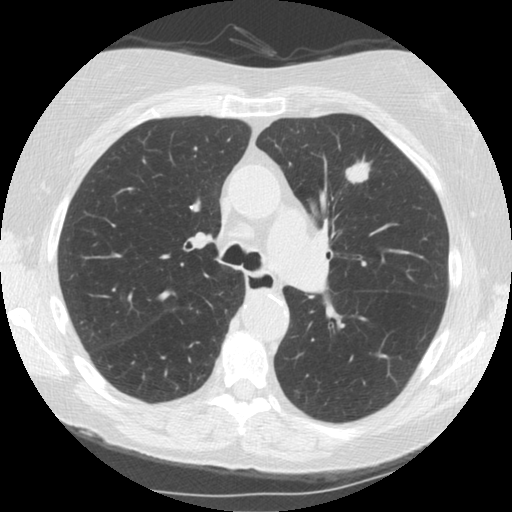
Low-dose screening chest CT, one axial slice. Position 96 of 153 along the scan axis. Reconstruction kernel STANDARD. 120 kVp. Lung window (W 1500 / L -600 HU). 2.5 mm slice thickness. 512 × 512 image matrix, field of view 330 × 330 mm.
Outlined on this slice (manually delineated by an expert):
- lesion 1 (tumor, upper lobe of left lung): bounding box <346,161,370,183> (left, top, right, bottom; pixels)